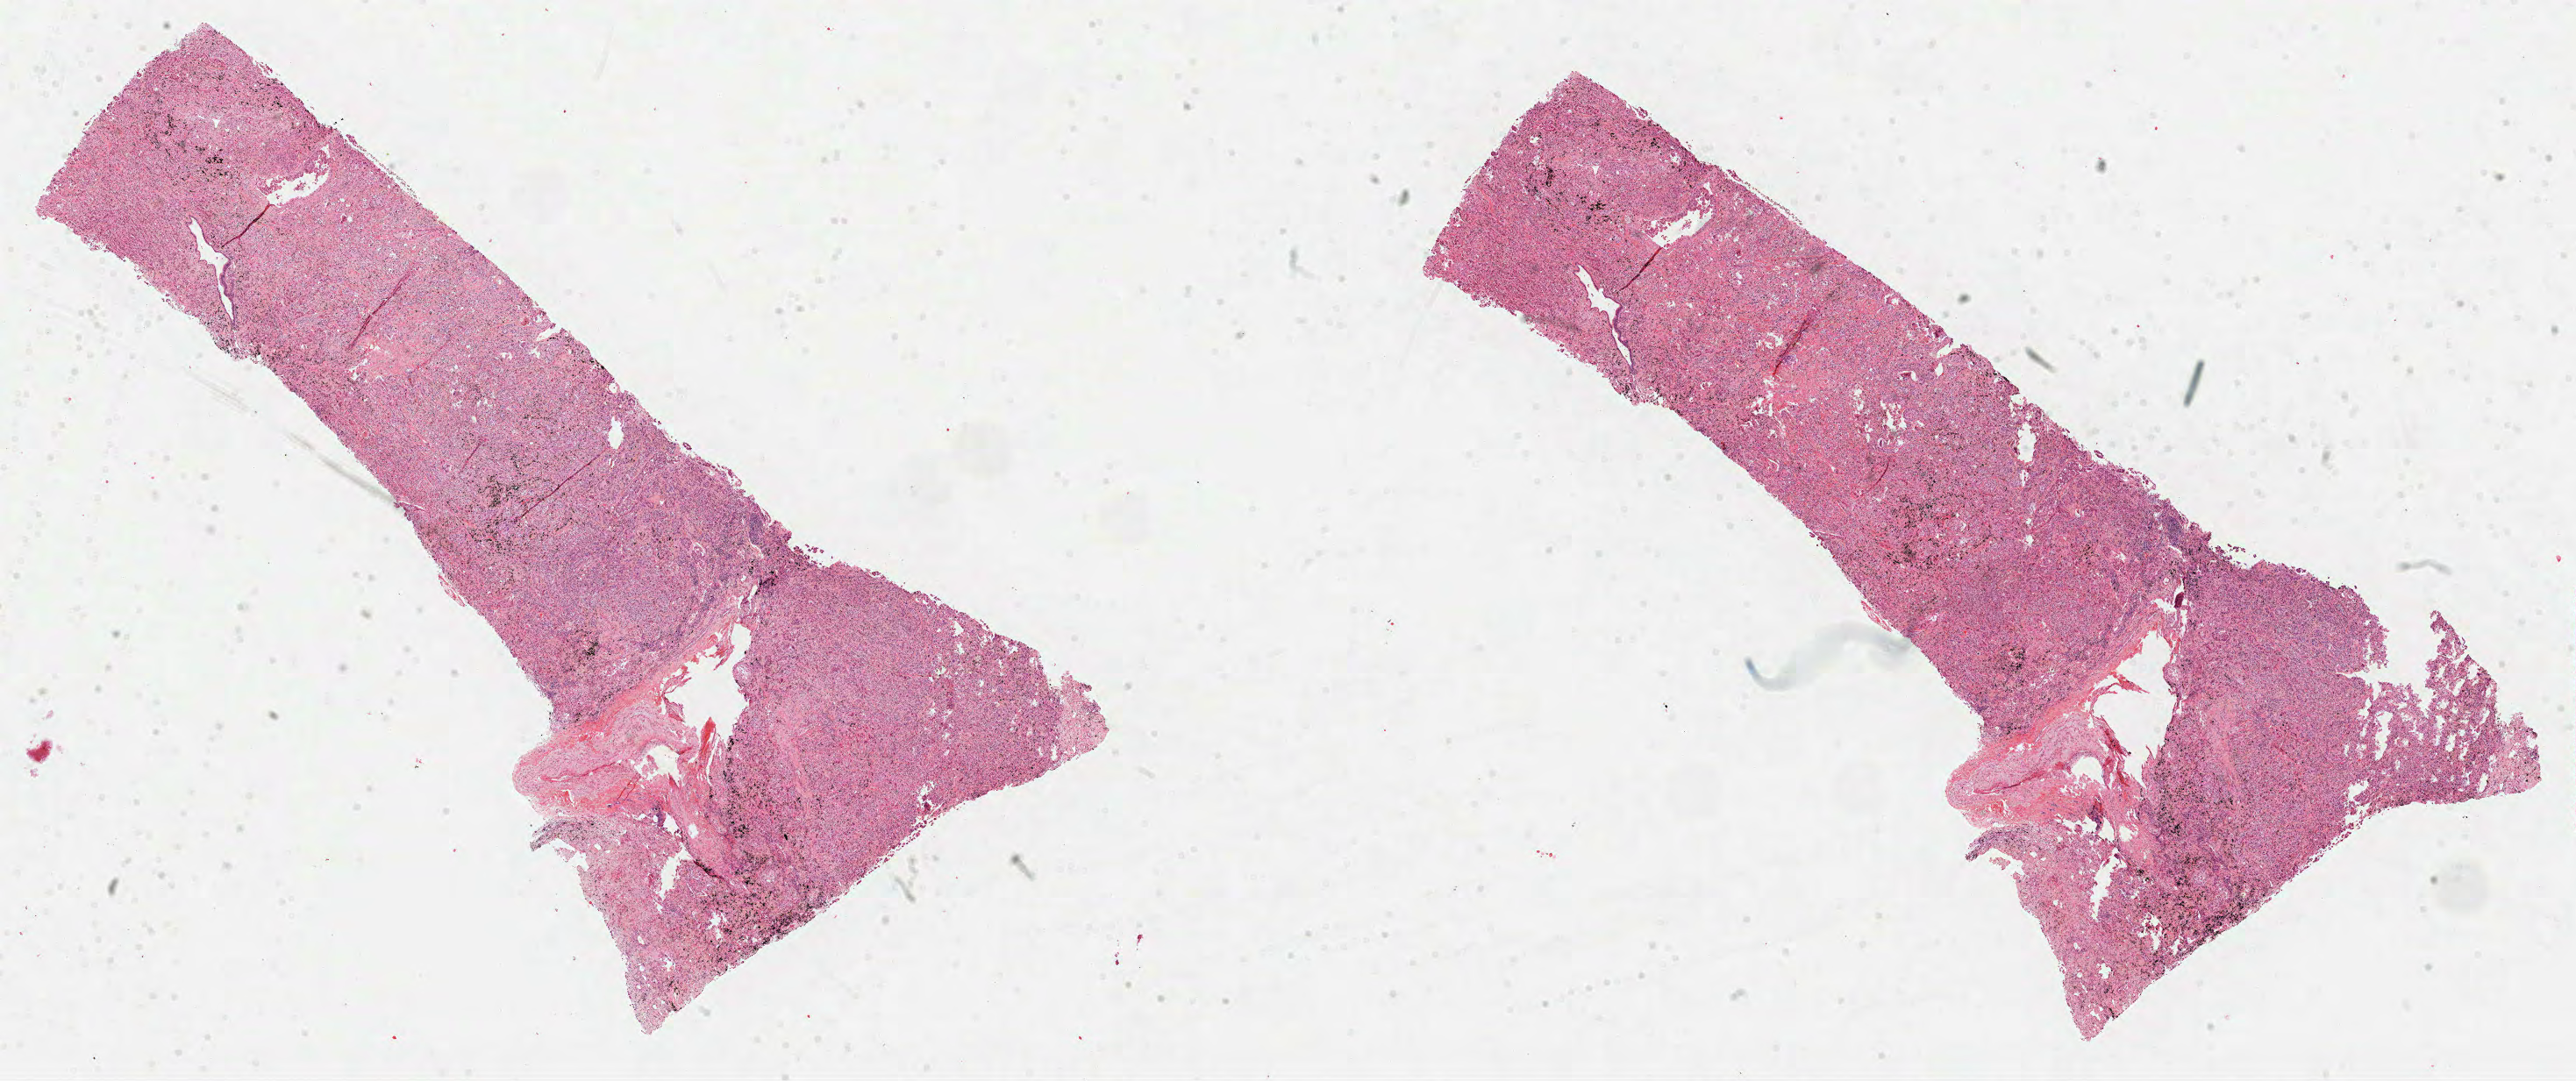
Whole-slide histology image, H&E-stained — shown as a low-resolution overview of the whole scanned area (about 23.7 x 9.9 mm, acquisition: 40x scan); formalin-fixed paraffin-embedded (FFPE) diagnostic section; lung, primary tumour sample. Female, age 72 years at initial diagnosis.
Histologic diagnosis: Adenocarcinoma, NOS (upper lobe, lung). Laterality: right. AJCC pathologic stage: IIIA (7th edition).